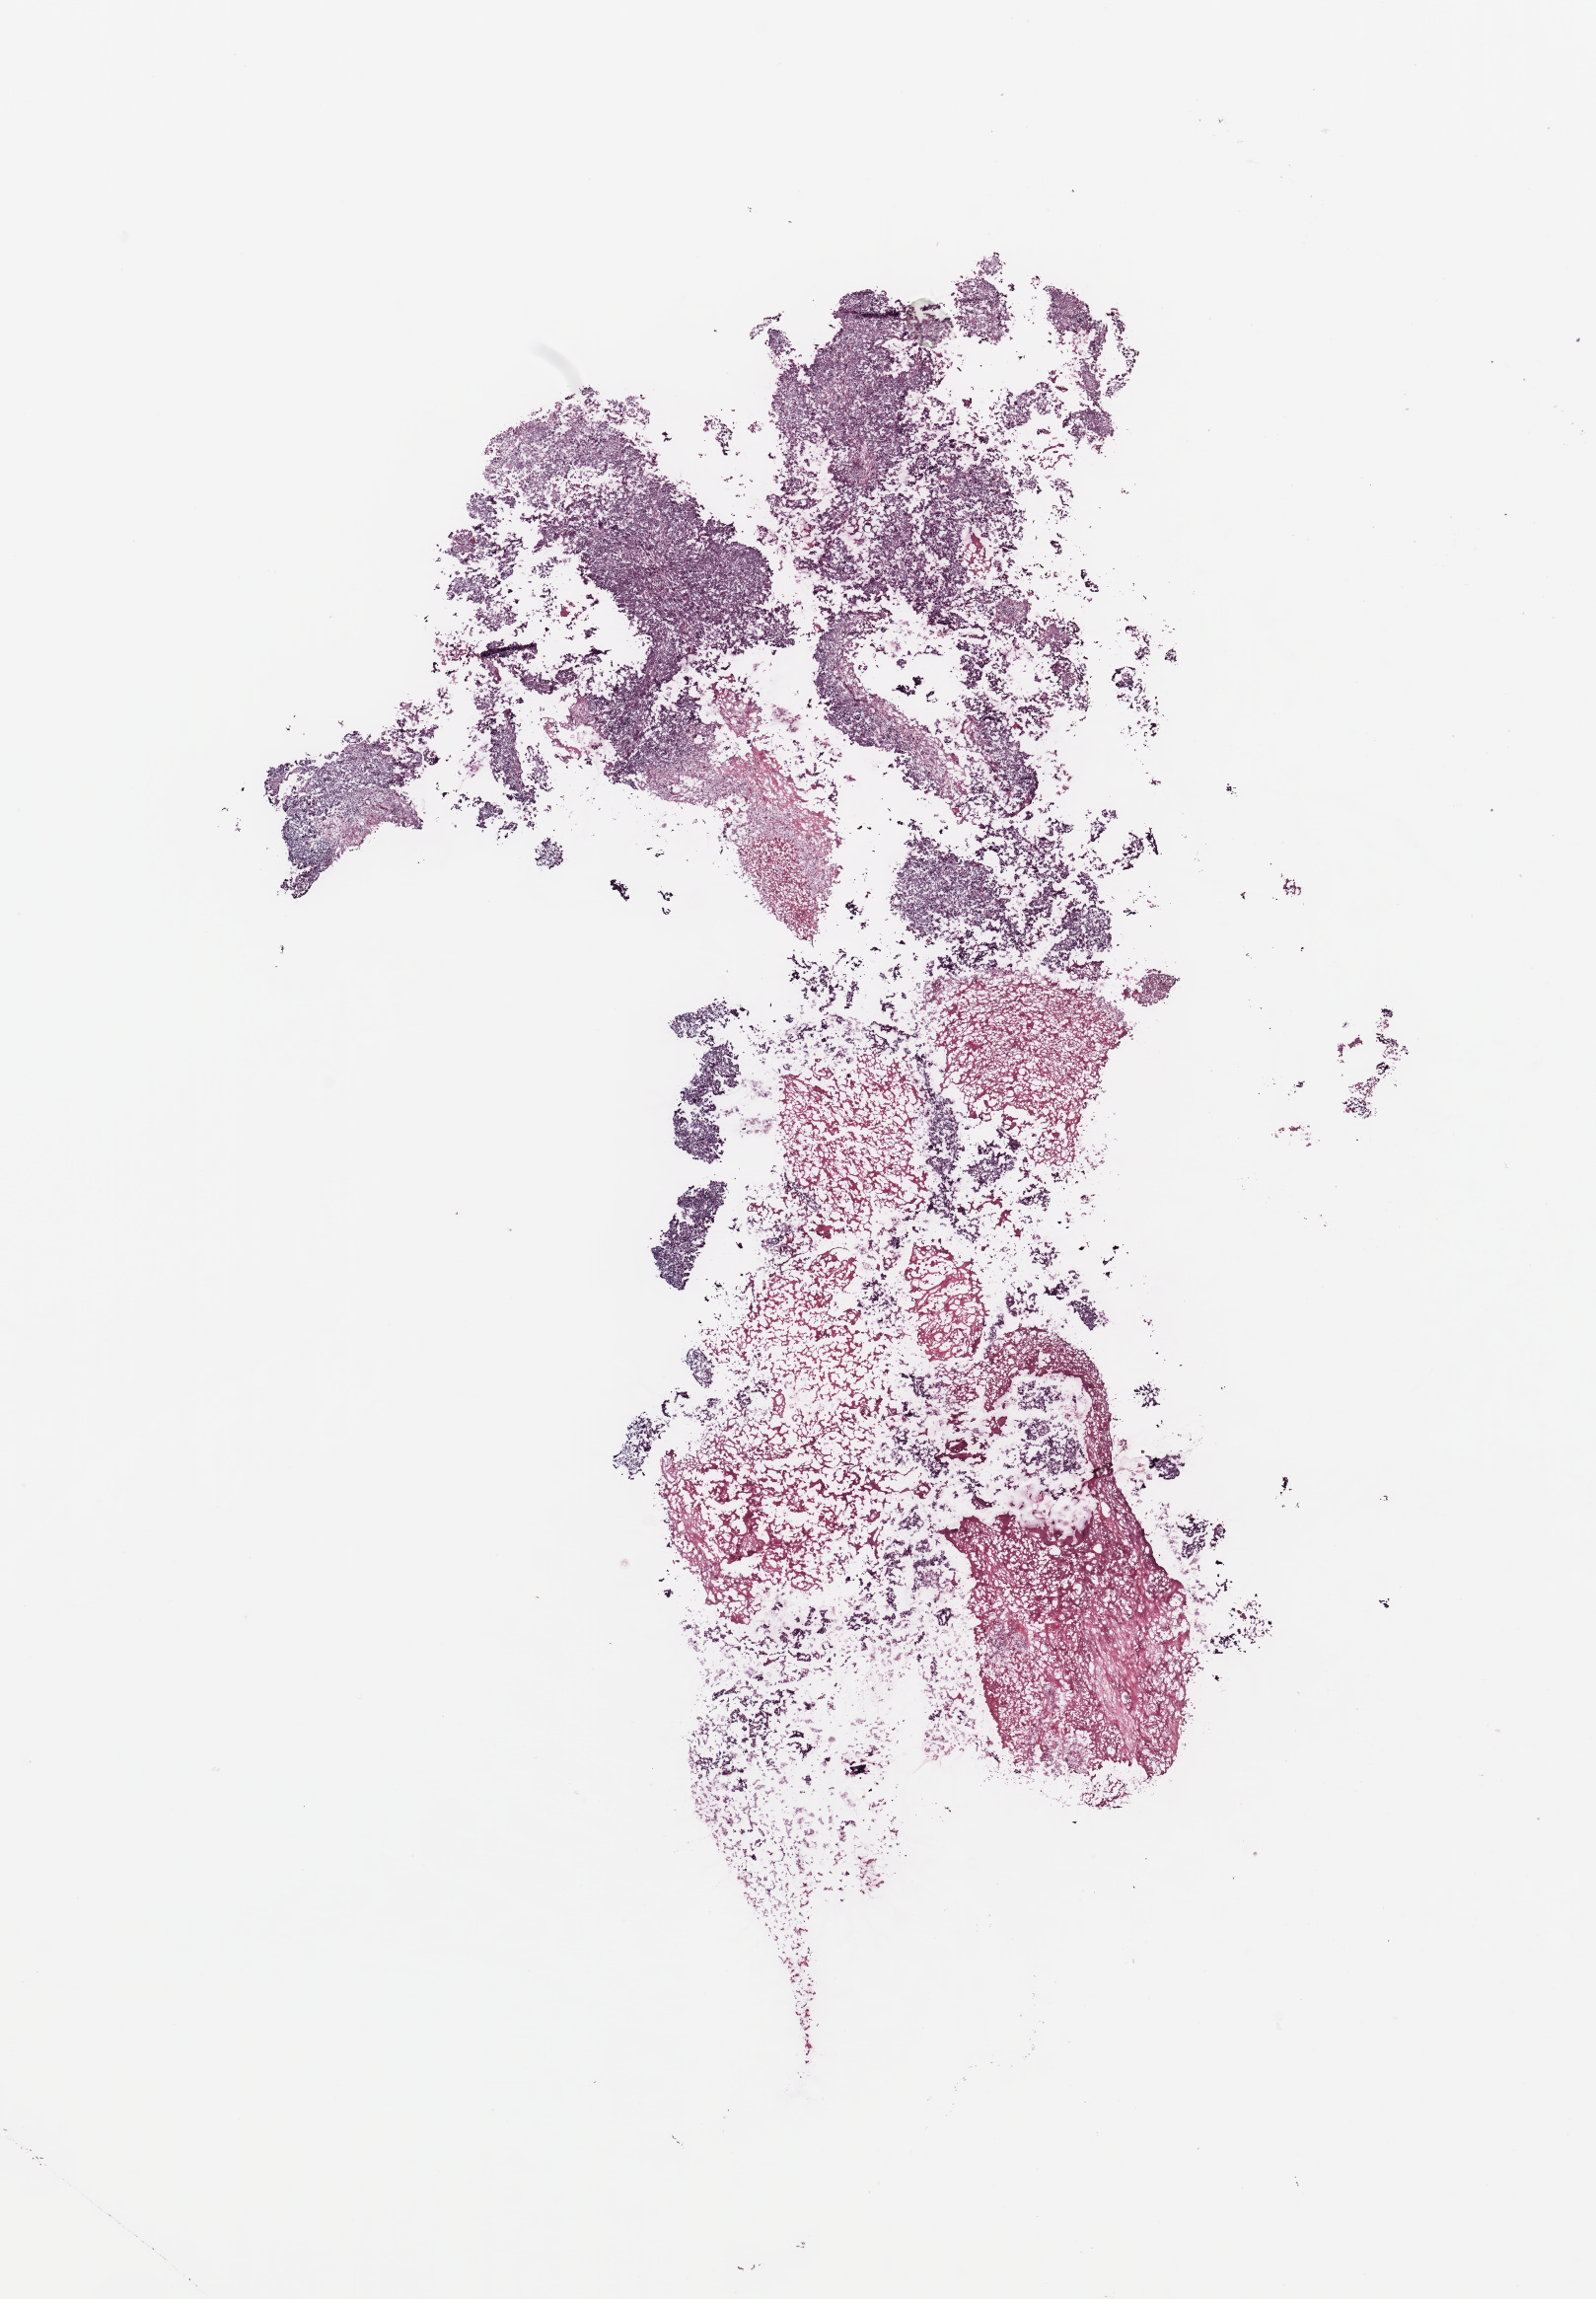
H&E-stained whole-slide image — a low-resolution overview of the entire scanned area, about 12.8 x 18.4 mm (from a 20x scan), breast, tumour tissue. Patient: female, age 58 years.
AJCC pathologic stage: II. Histologic diagnosis: Infiltrating duct carcinoma, NOS.